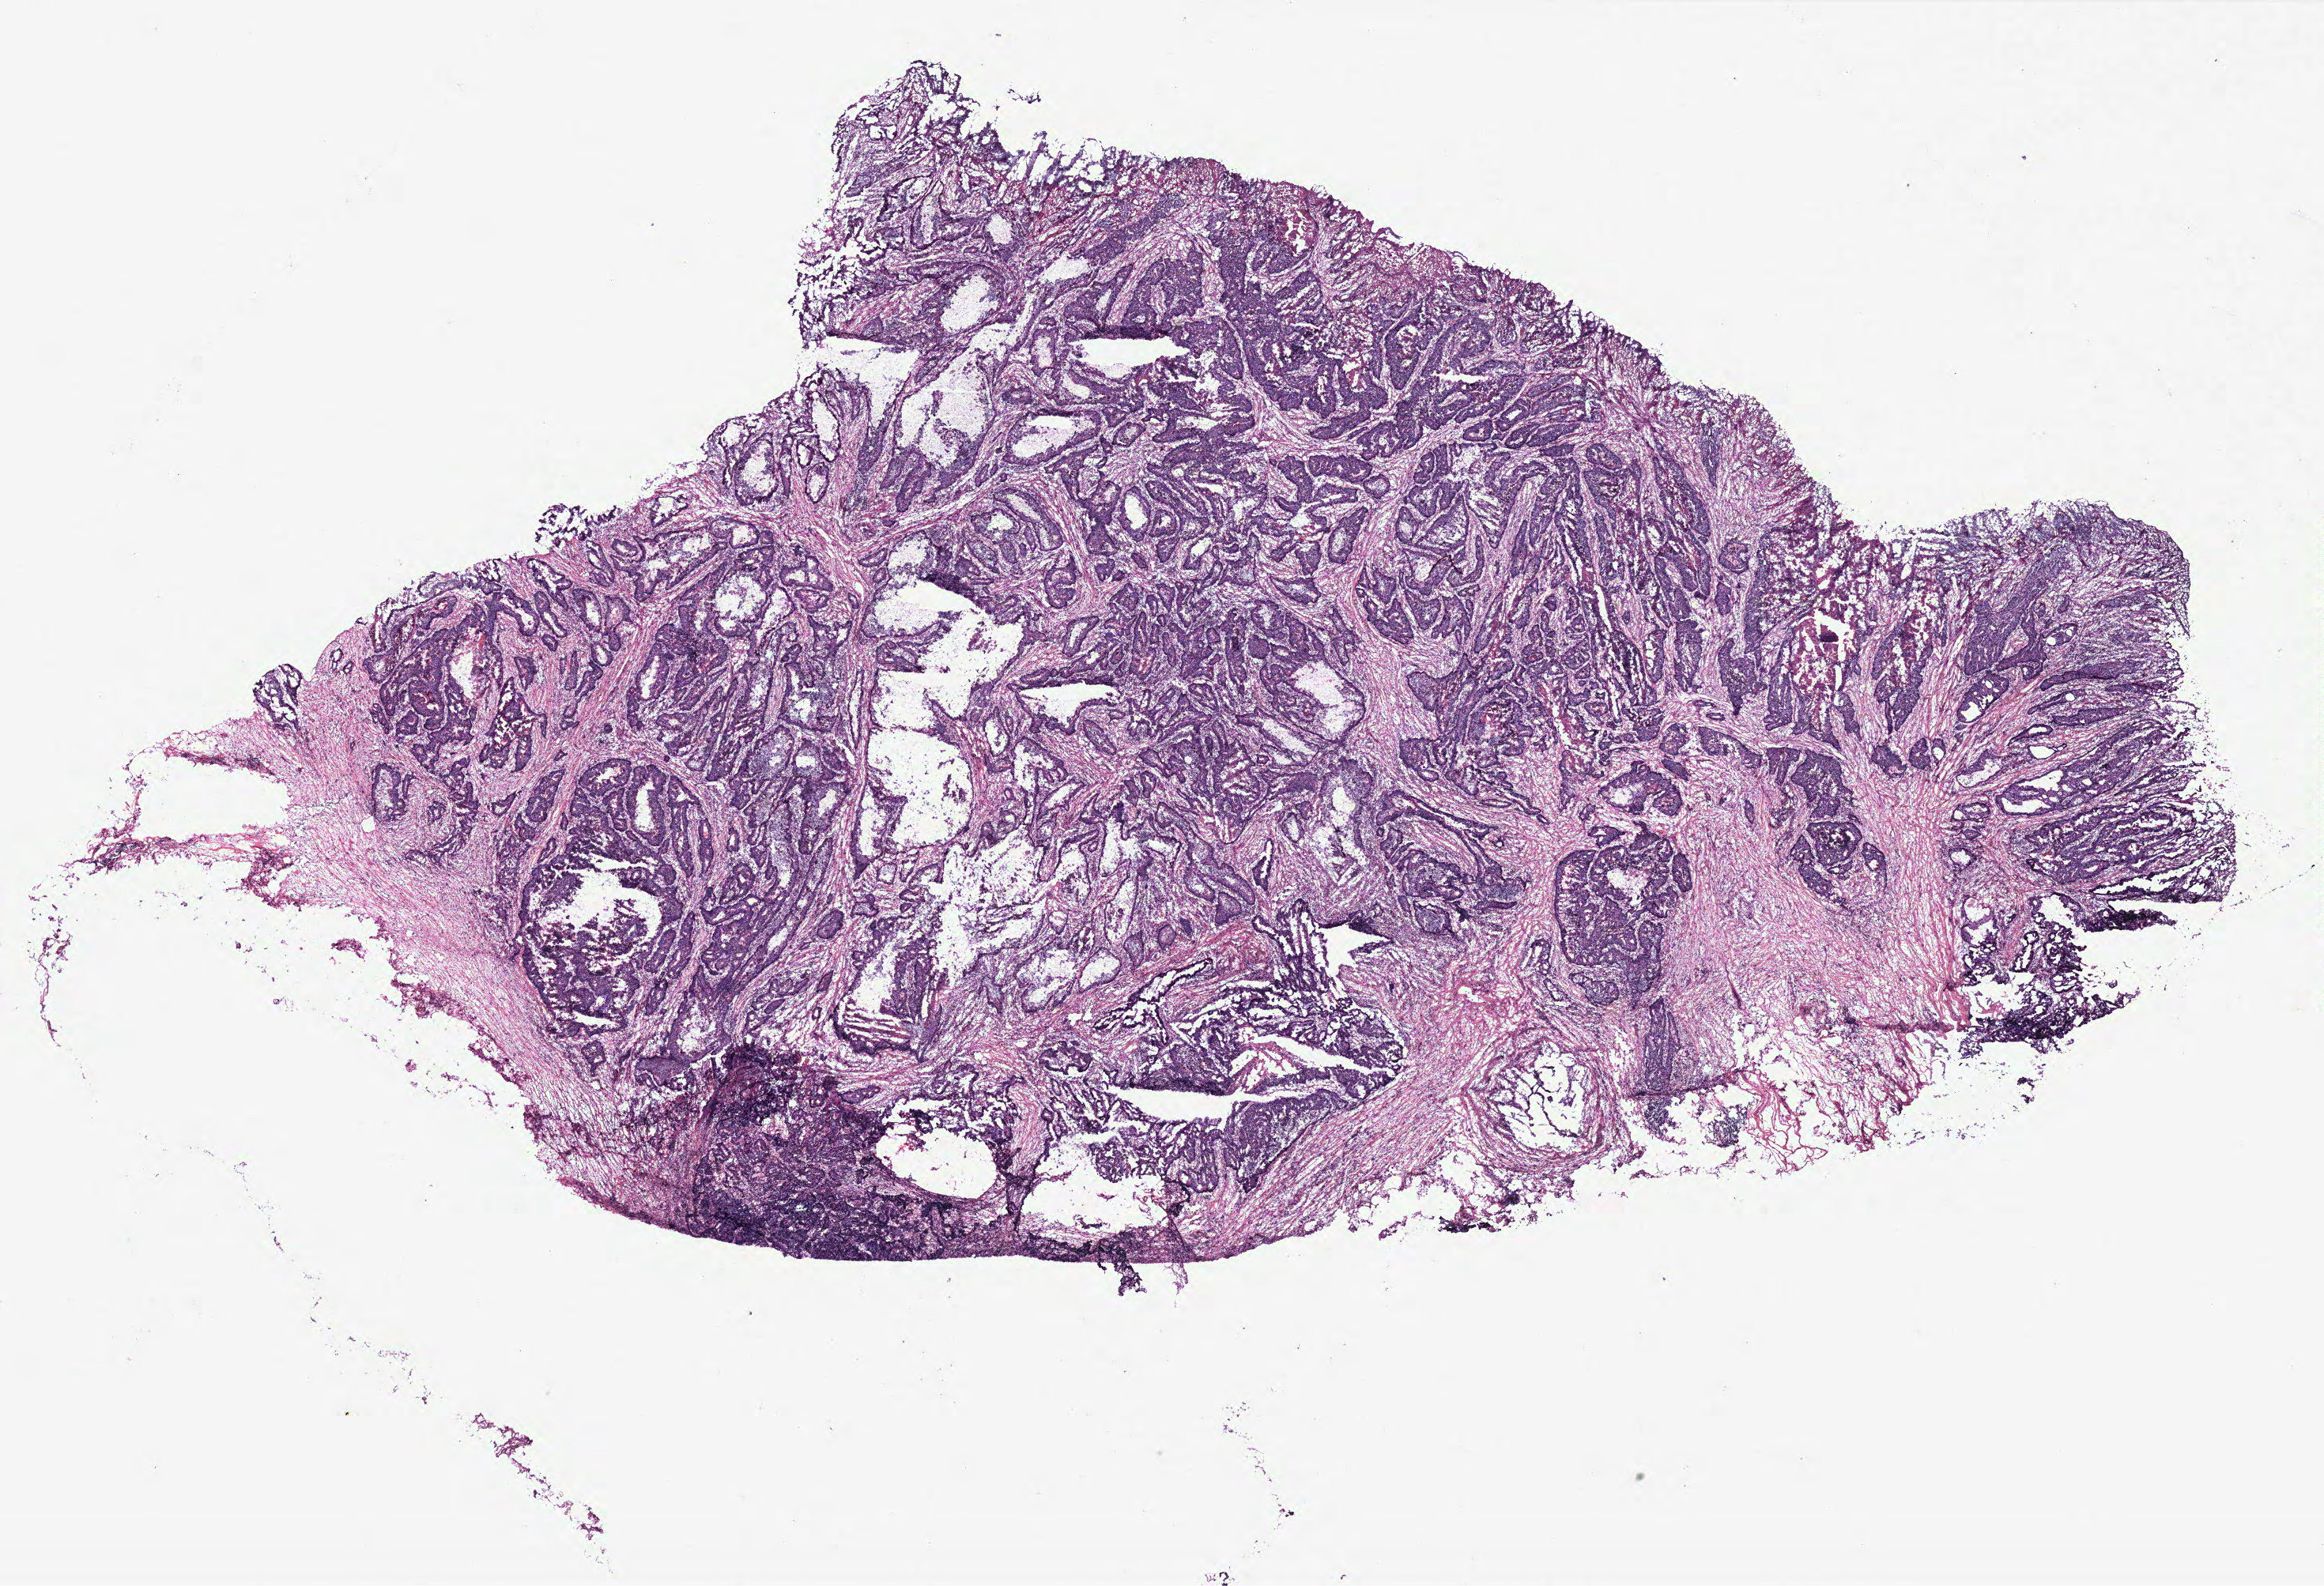
H&E whole-slide image — a low-resolution overview of the entire scanned area, about 23.5 x 16.1 mm; tumour tissue sample, colon. Patient: female, age 69 years.
Diagnosis: Adenocarcinoma, NOS. Primary tumour site (as recorded): colon. AJCC pathologic stage: IVA.